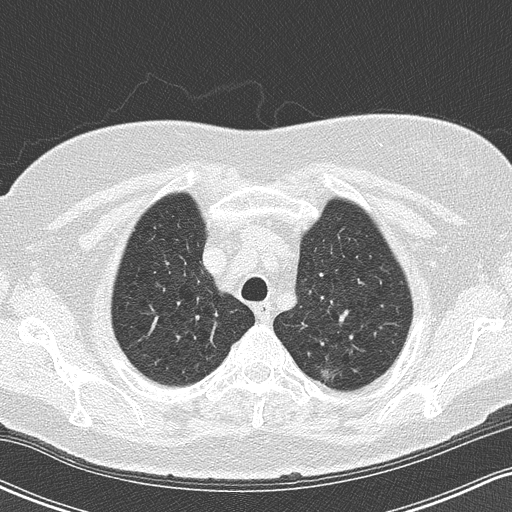
Chest CT (low-dose screening protocol), one axial image. Third screening round (two years after baseline). Lung window (W 1500 / L -600 HU). 2 mm slice thickness. Female participant, aged 65 years at enrolment. Former smoker at enrolment.
Expert-annotated lung lesion, bounding box (x1, y1, x2, y2) in pixels: (309, 350, 349, 395). The exam's reader record, not a measurement of the box and not confirmed to be the same lesion: non-calcified nodule or mass ≥4 mm, left upper lobe, 8 × 6 mm, pre-existing on the prior screen: yes.